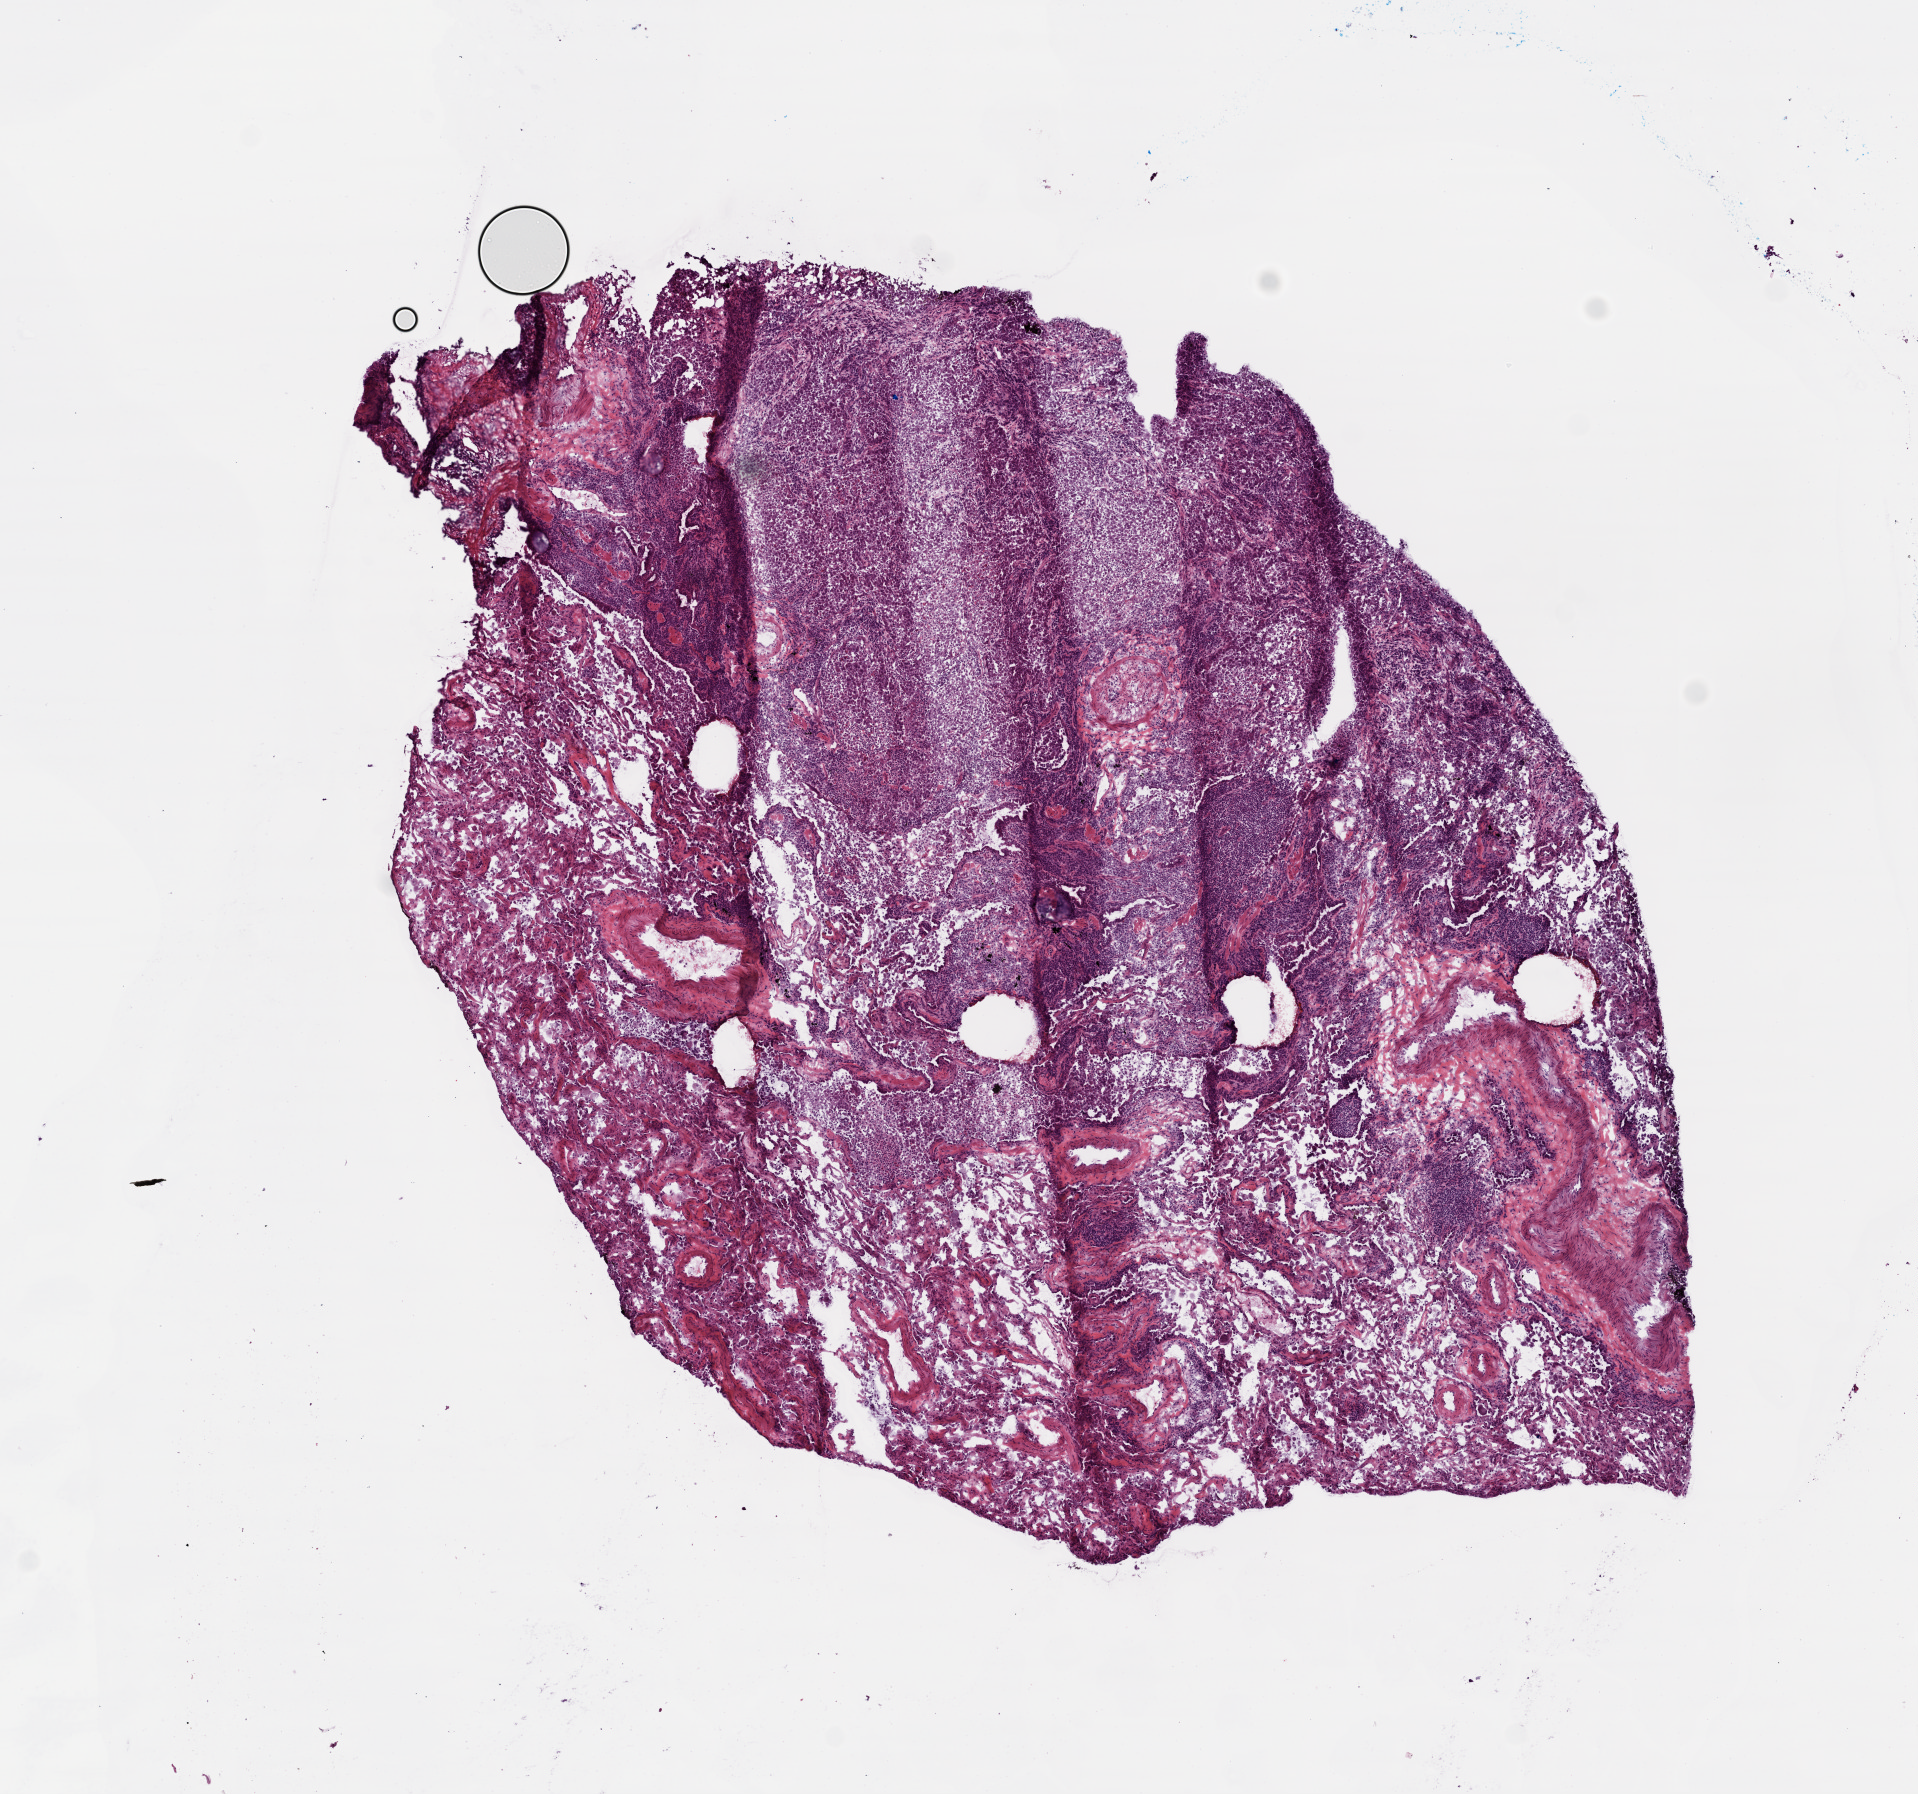
Whole-slide histology image, H&E — whole scanned area (about 7.7 x 7.2 mm) shown as a low-resolution overview. Frozen section from the top of the tissue portion. Lung, primary tumour sample. Male patient; age at initial diagnosis 77 years. Slide review estimates, as recorded: tumour cells 98%, tumour nuclei 65%, normal cells 0%, stromal cells 1%, necrosis 1%.
- laterality: left
- AJCC pathologic stage: IA
- pathologic diagnosis: Adenocarcinoma, NOS (lower lobe, lung)